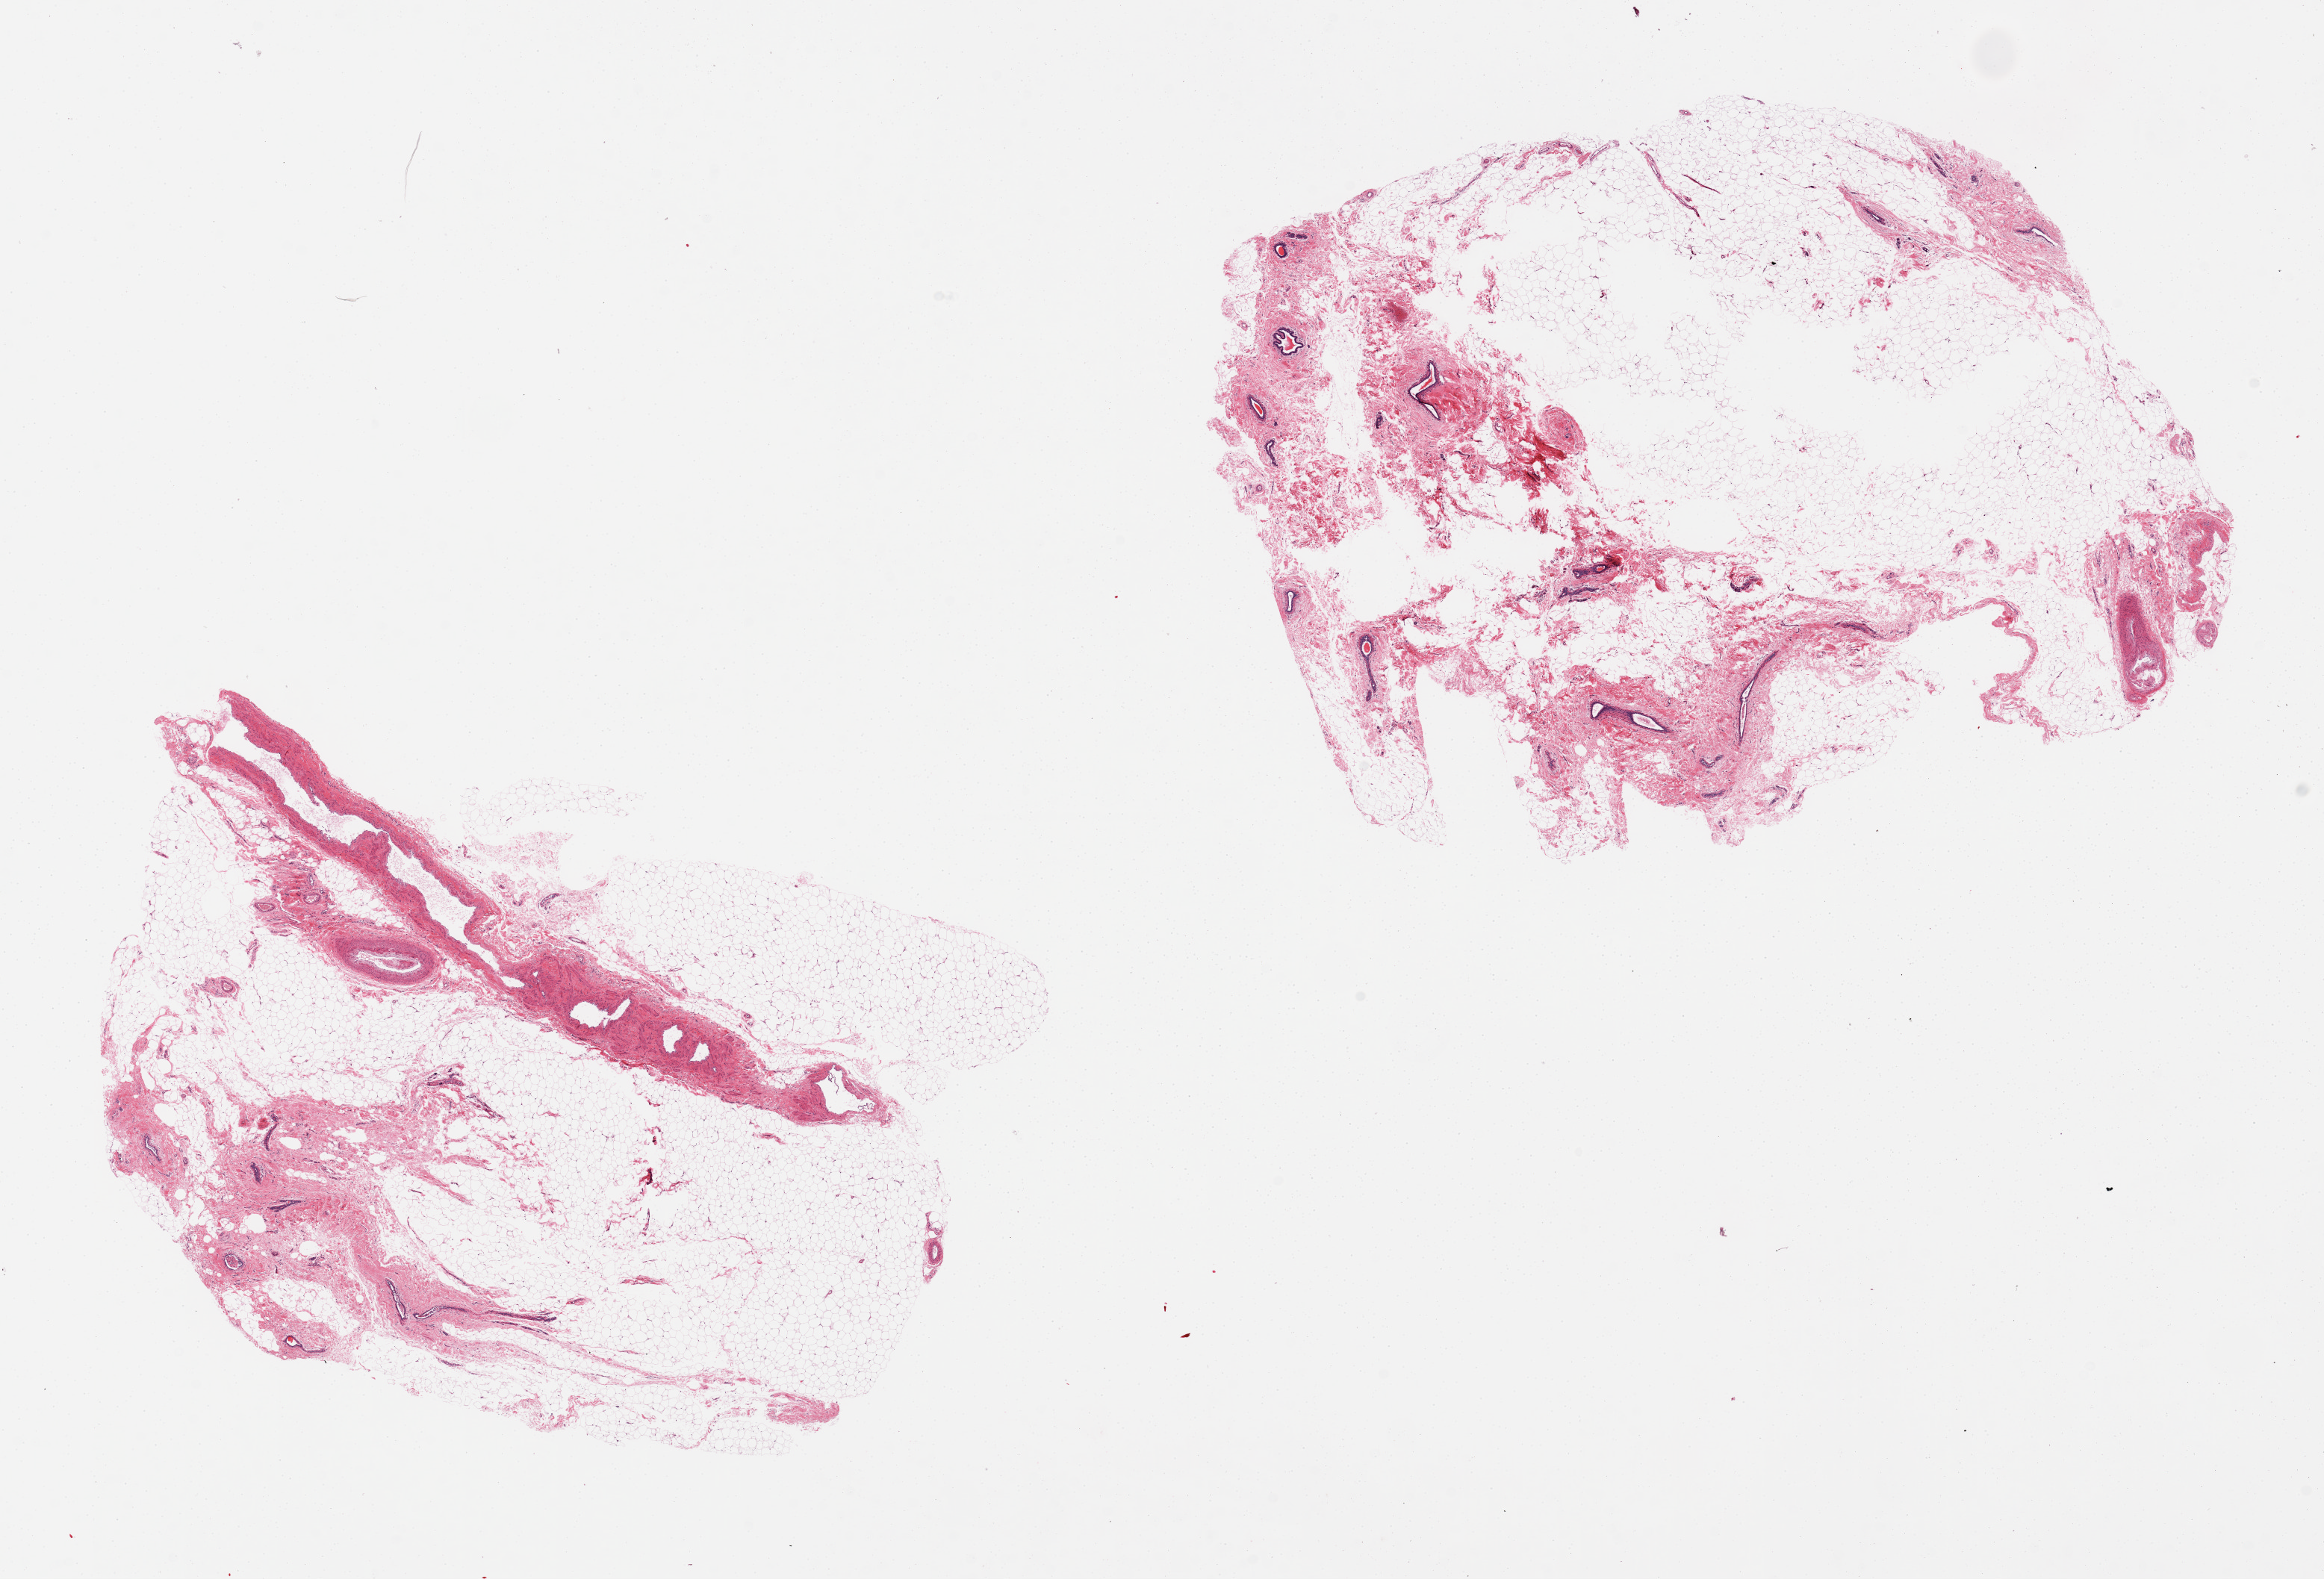
Digitized haematoxylin and eosin-stained section, shown as a low-resolution overview of the whole scanned area (about 24.6 x 16.7 mm, from a 20x scan), PAXgene-fixed paraffin-embedded (PFPE) section, sampled site (target tissue): breast, donor tissue sample. Female donor.
Pathologist's review note for this sample: 2 pieces, predominantly fat with ~10% fibrous stroma and few ductal elements.